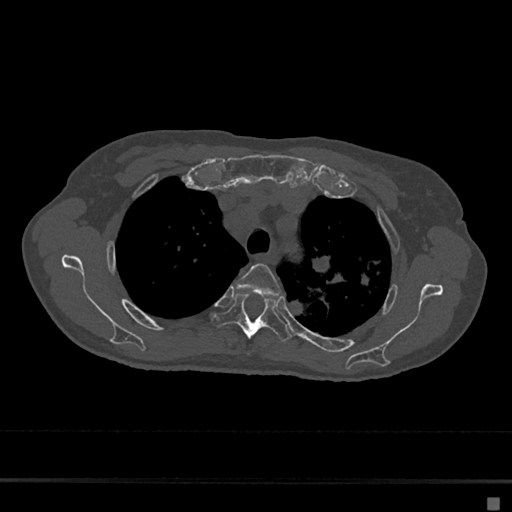
CT including the spine, one axial slice. Position 514 of 797 along the scan axis. Reconstruction kernel Br40s/3. 120 kVp. Bone window (W 1800 / L 400 HU). 0.5 mm slice thickness. 512 × 512 image matrix, field of view 360 × 360 mm. Female patient, age 68 years. Case-level facts recorded for this patient, not image findings: primary cancer: renal.
Annotated regions visible in this slice (semi-automatically segmented with operator editing):
- T3 vertebra: bounding box (x1, y1, x2, y2) in pixels: (236, 263, 280, 297)
- T4 vertebra: (211, 295, 291, 341)